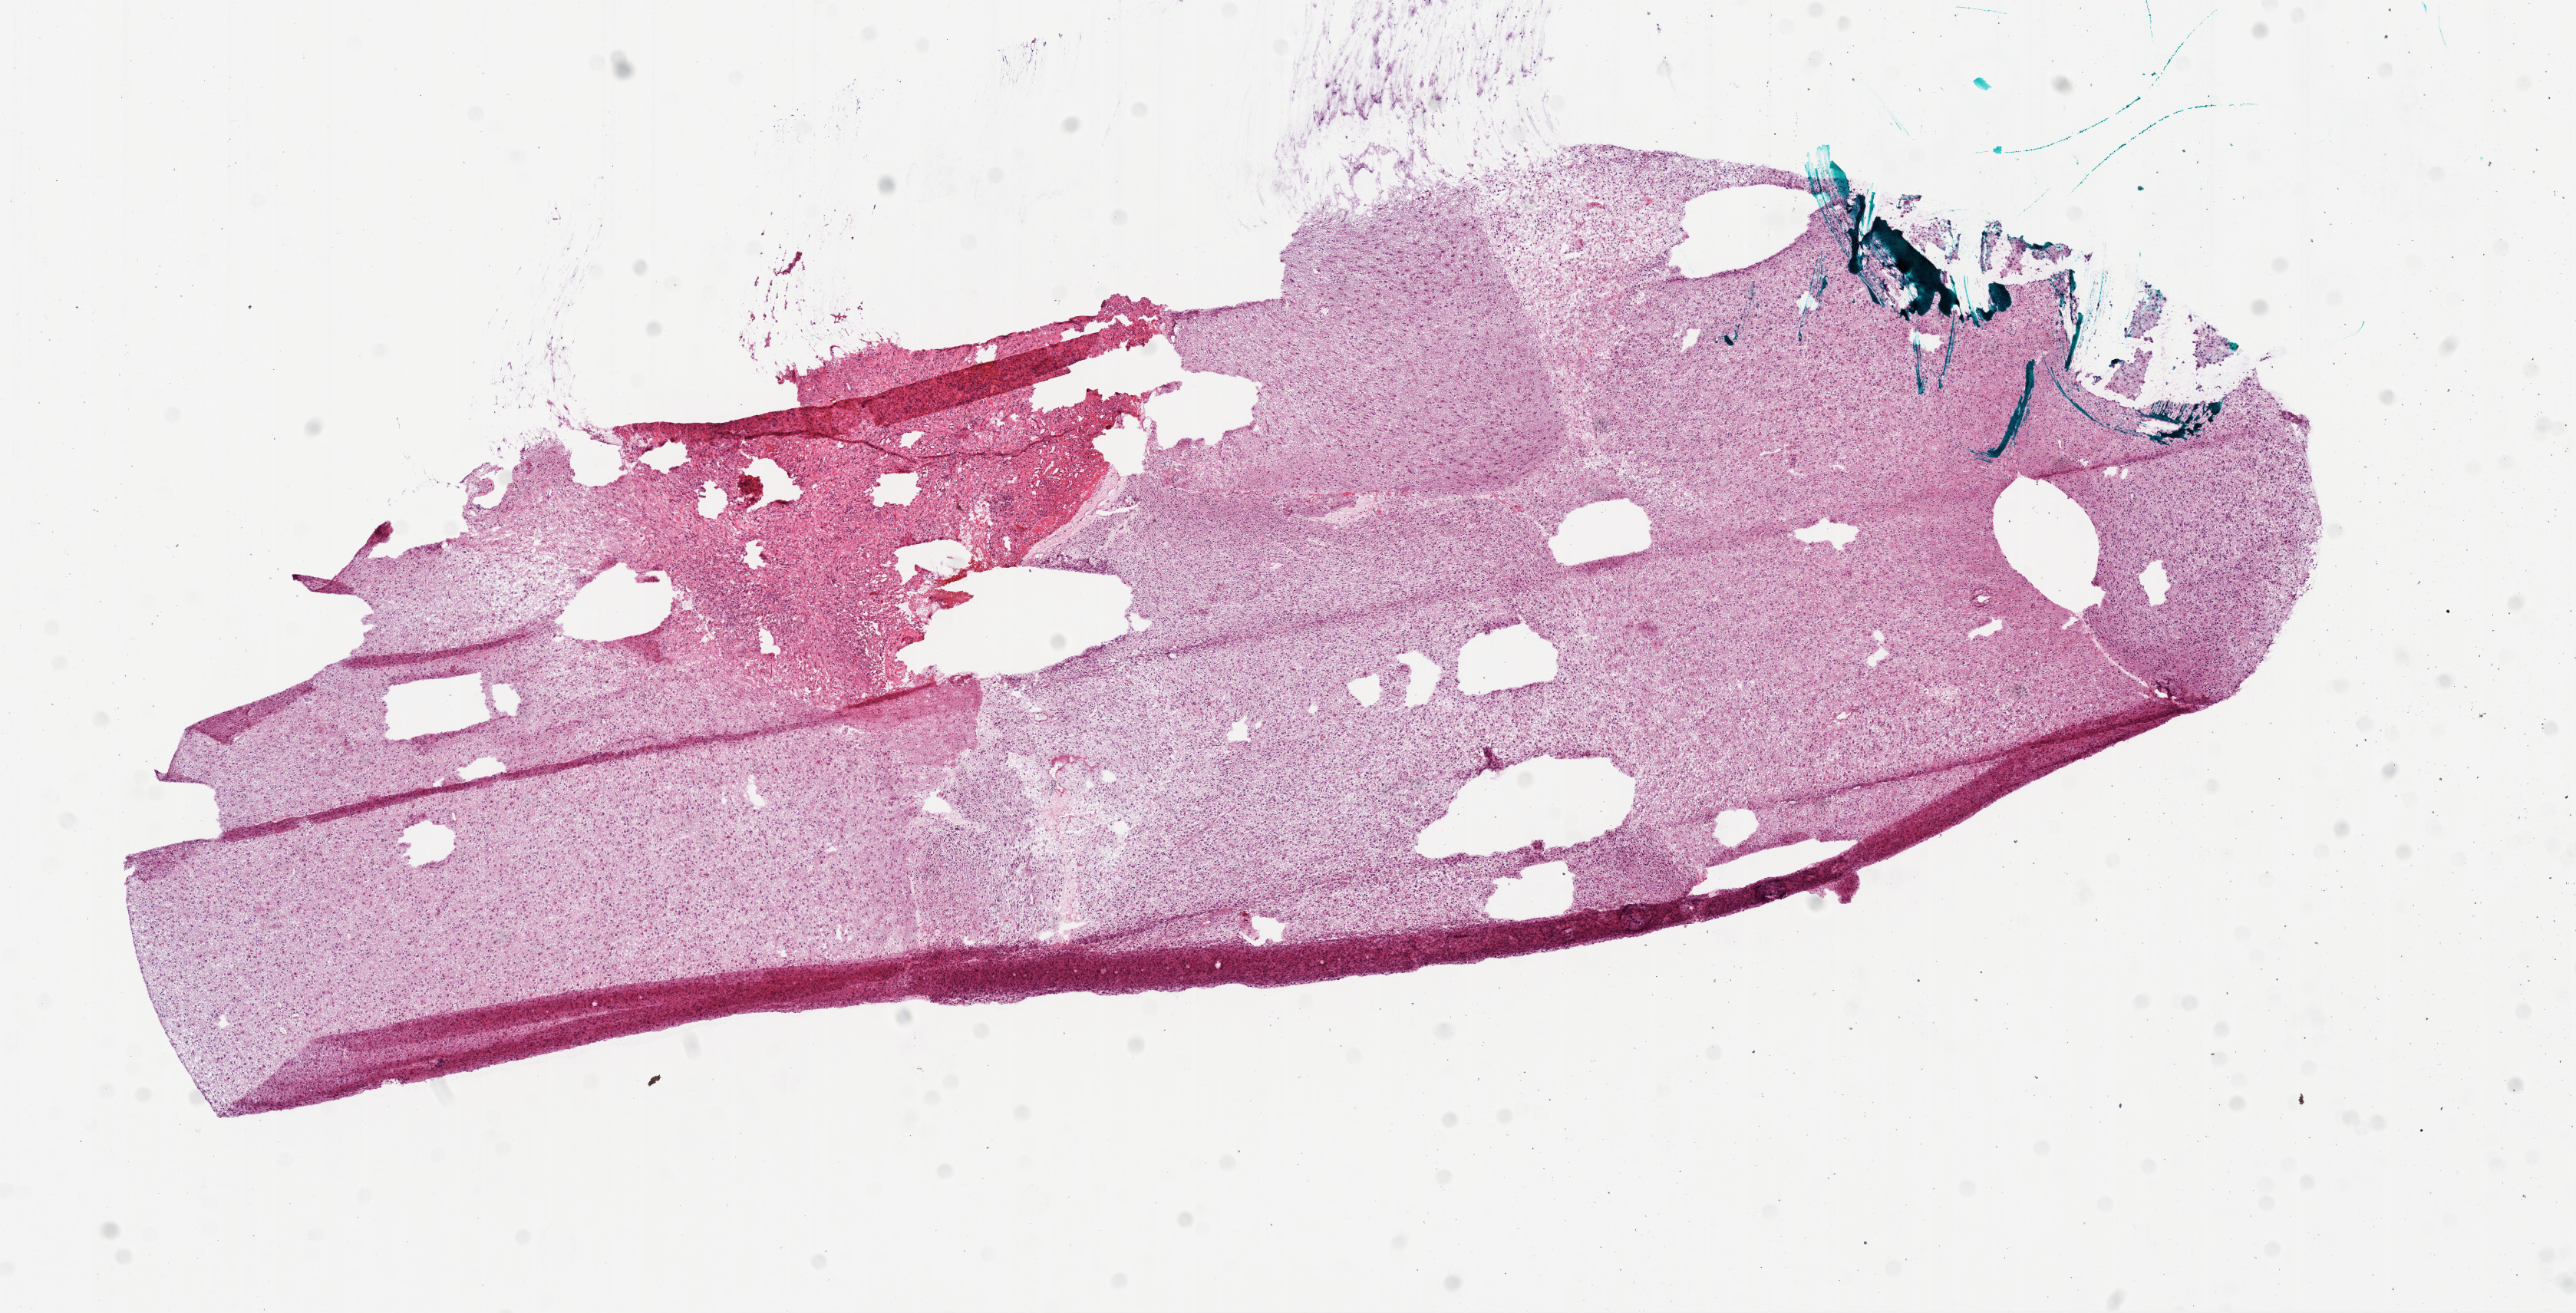
H&E whole-slide image, whole scanned area (about 13.5 x 6.9 mm, slide scanned at 20x) shown as a low-resolution overview; frozen section from the bottom of the tissue portion; primary tumour sample from the brain. Male patient; age at initial diagnosis 69 years.
Pathologic diagnosis: Glioblastoma.